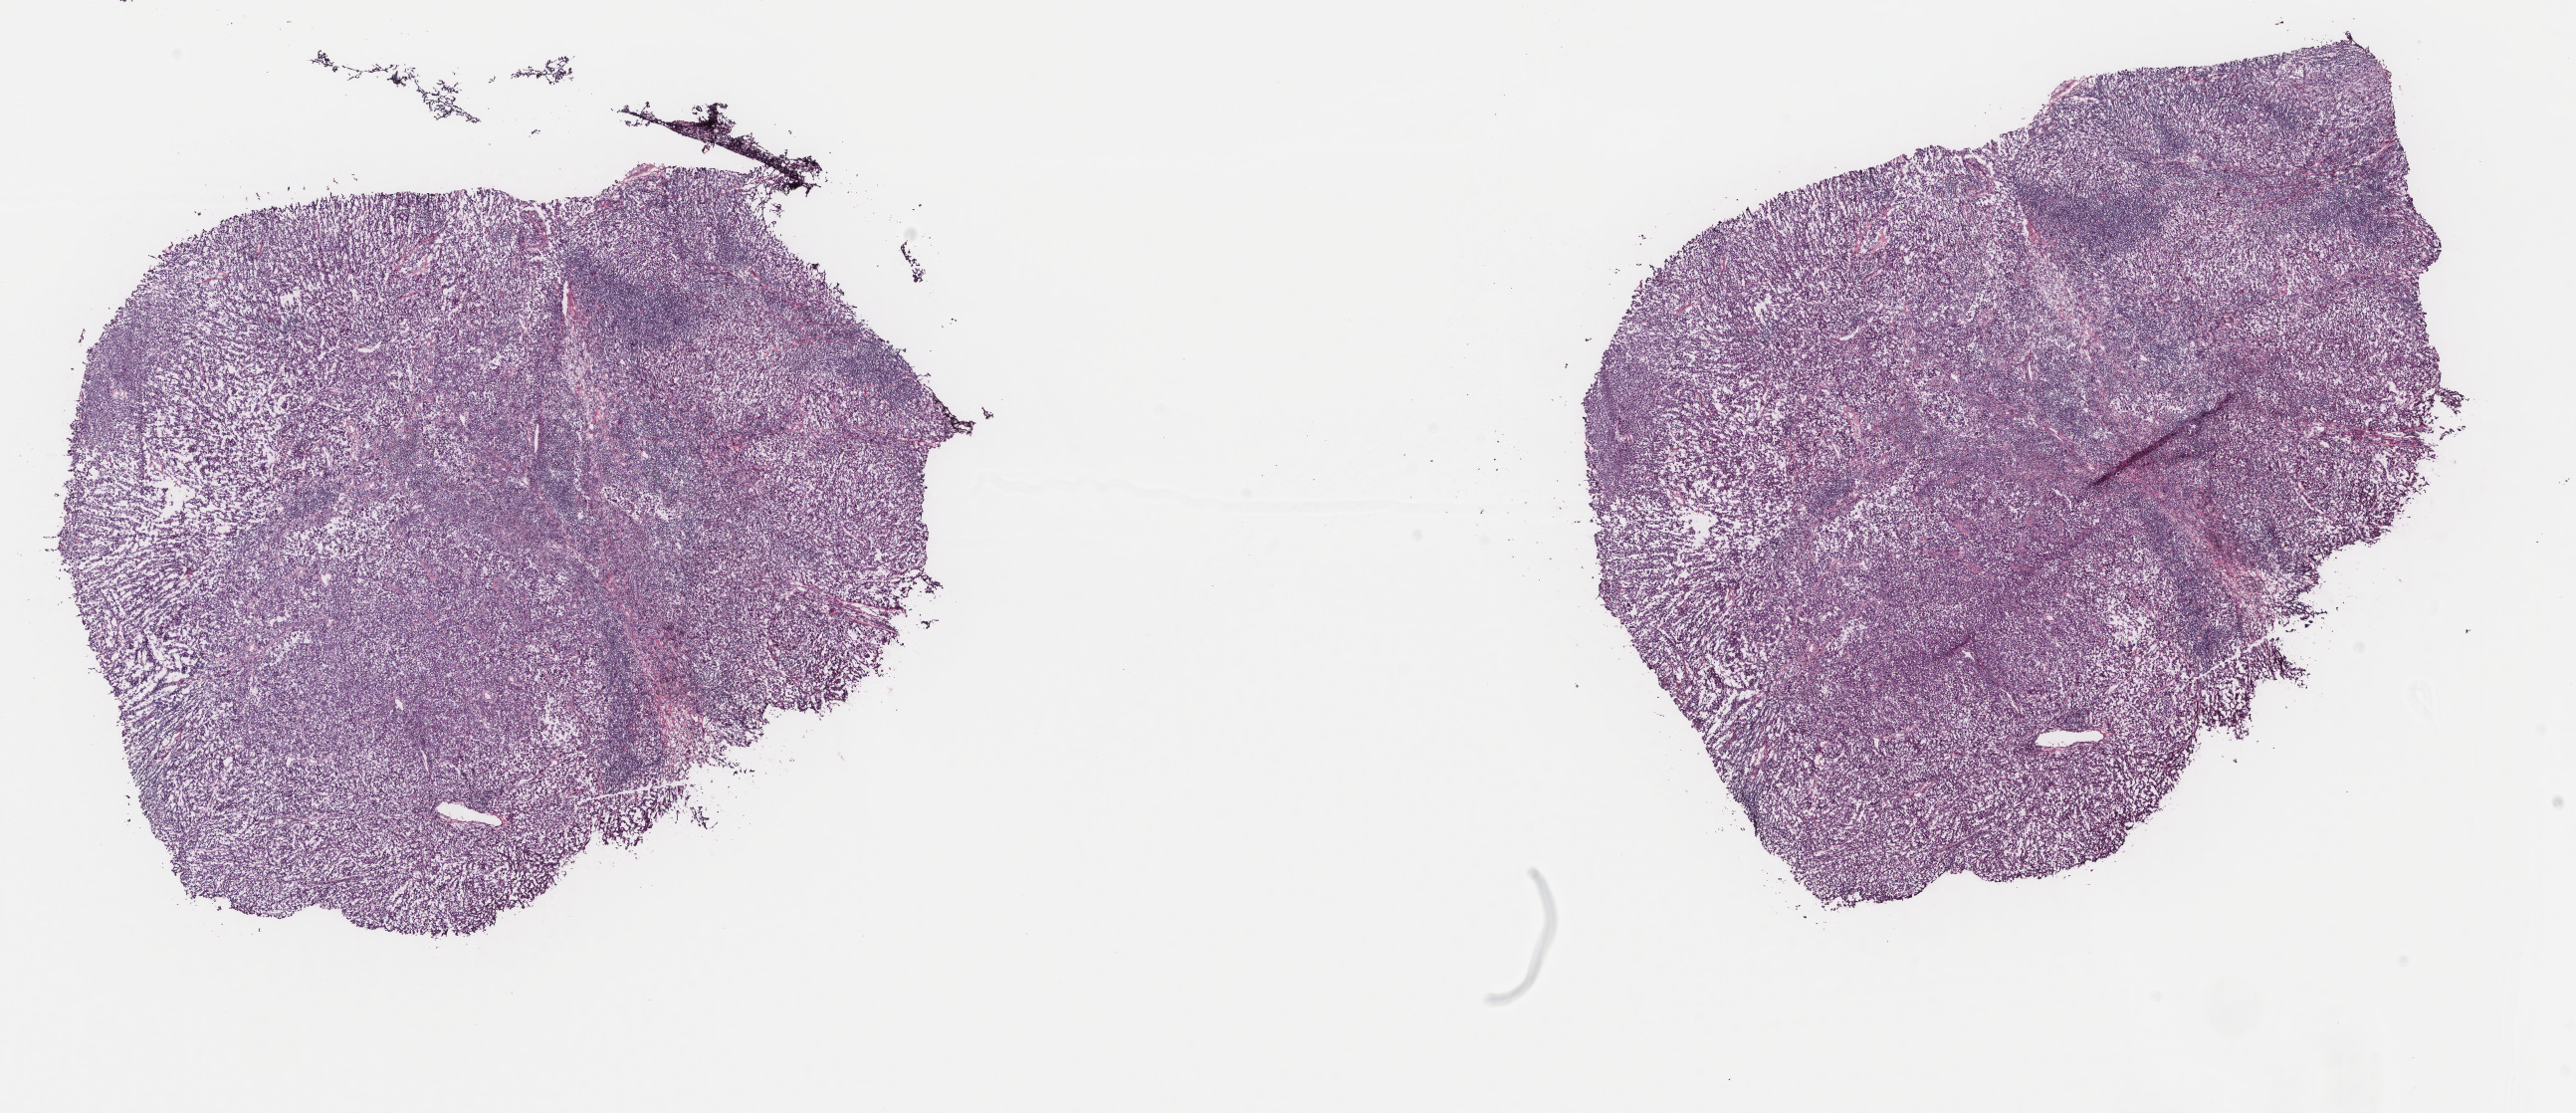
Digitized H&E-stained tissue section (whole slide) — shown as a low-resolution overview of the whole scanned area (about 20.5 x 8.9 mm, acquisition: 40x scan), frozen section from the top of the tissue portion, metastatic tumour sample, sampled site not recorded. Male patient; age at initial diagnosis 51 years. Pathologist review of this section (percent, as recorded): tumour cells 100%, tumour nuclei 85%, normal cells 0%, stromal cells 0%, necrosis 0%. Infiltration values recorded for this section: lymphocyte infiltration 0%, monocyte infiltration 0%, neutrophil infiltration 0%.
This section: metastatic tumour tissue. Patient diagnosis: Malignant melanoma, NOS.